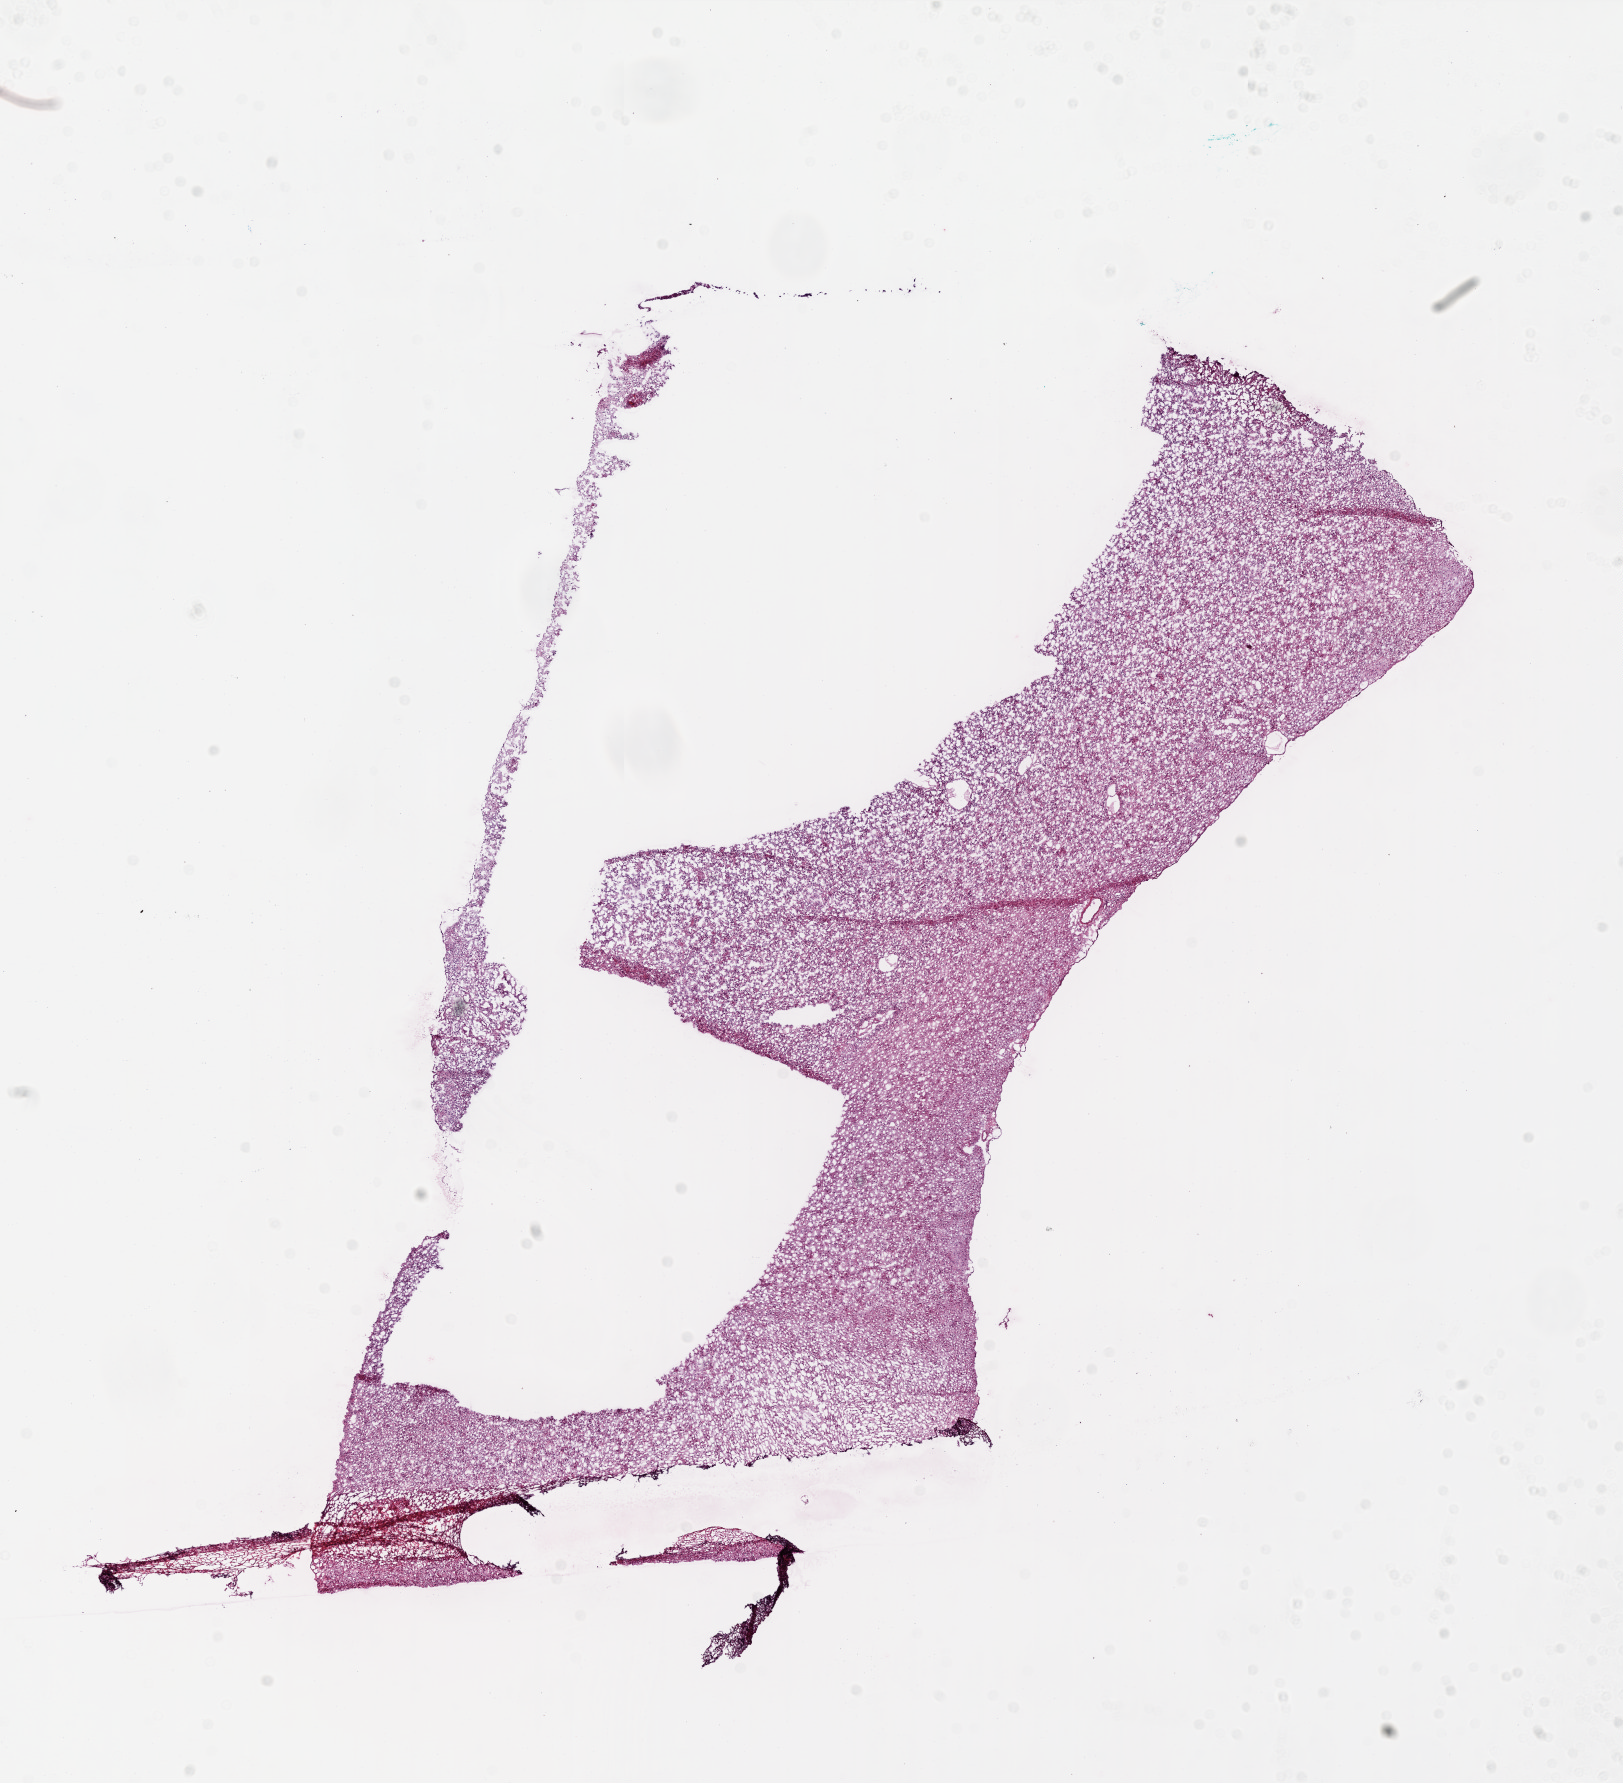
Whole-slide histology image, H&E-stained, whole scanned area (about 13.0 x 14.3 mm, from a 20x scan) shown as a low-resolution overview; frozen section from the bottom of the tissue portion; primary tumour sample from the brain. Patient: male, age at initial diagnosis 68 years. Slide review estimates, as recorded: tumour cells 100%, tumour nuclei 100%, normal cells 0%, stromal cells 0%, necrosis 0%. Inflammatory infiltration, as recorded: lymphocyte infiltration 0%.
Diagnosis: Glioblastoma.